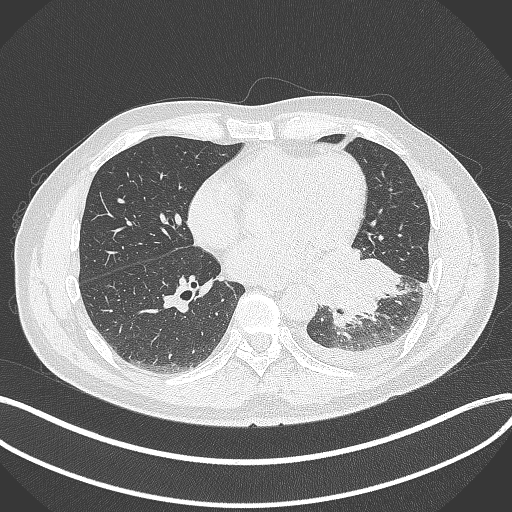
Chest CT, one axial slice. Slice 149 of 342 in the series (ordered by position). Lung window (W 1500 / L -600 HU). 1 mm slice thickness. 512 × 512 image matrix. Patient: male, 58 years. Case-level facts recorded for this patient, not image findings: clinical TNM (as recorded): T3 N1 M1b.
Annotated regions visible in this slice (bounding box drawn by a radiologist):
- lung tumour (recorded histology: small cell carcinoma): box from (x=311, y=242) to (x=405, y=331) px